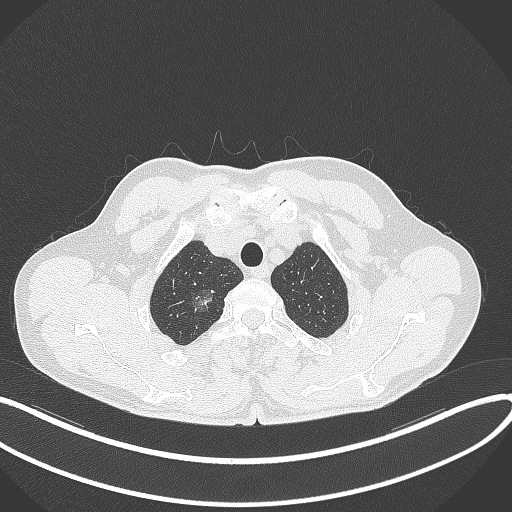
Chest CT, one axial slice; slice 338 of 407 in the series (ordered by position); reconstruction kernel B70f; 120 kVp; lung window (W 1500 / L -600 HU); 1 mm slice thickness; 512 × 512 image matrix, field of view 400 × 400 mm. Patient: male, 58 years. From the clinical record (not read from this slice): clinical TNM (as recorded): T1c N0 M0.
Structures marked on this image (bounding box drawn by a radiologist):
- lung tumour (recorded histology: adenocarcinoma): bounding box [x1, y1, x2, y2] px = [190, 284, 222, 318]